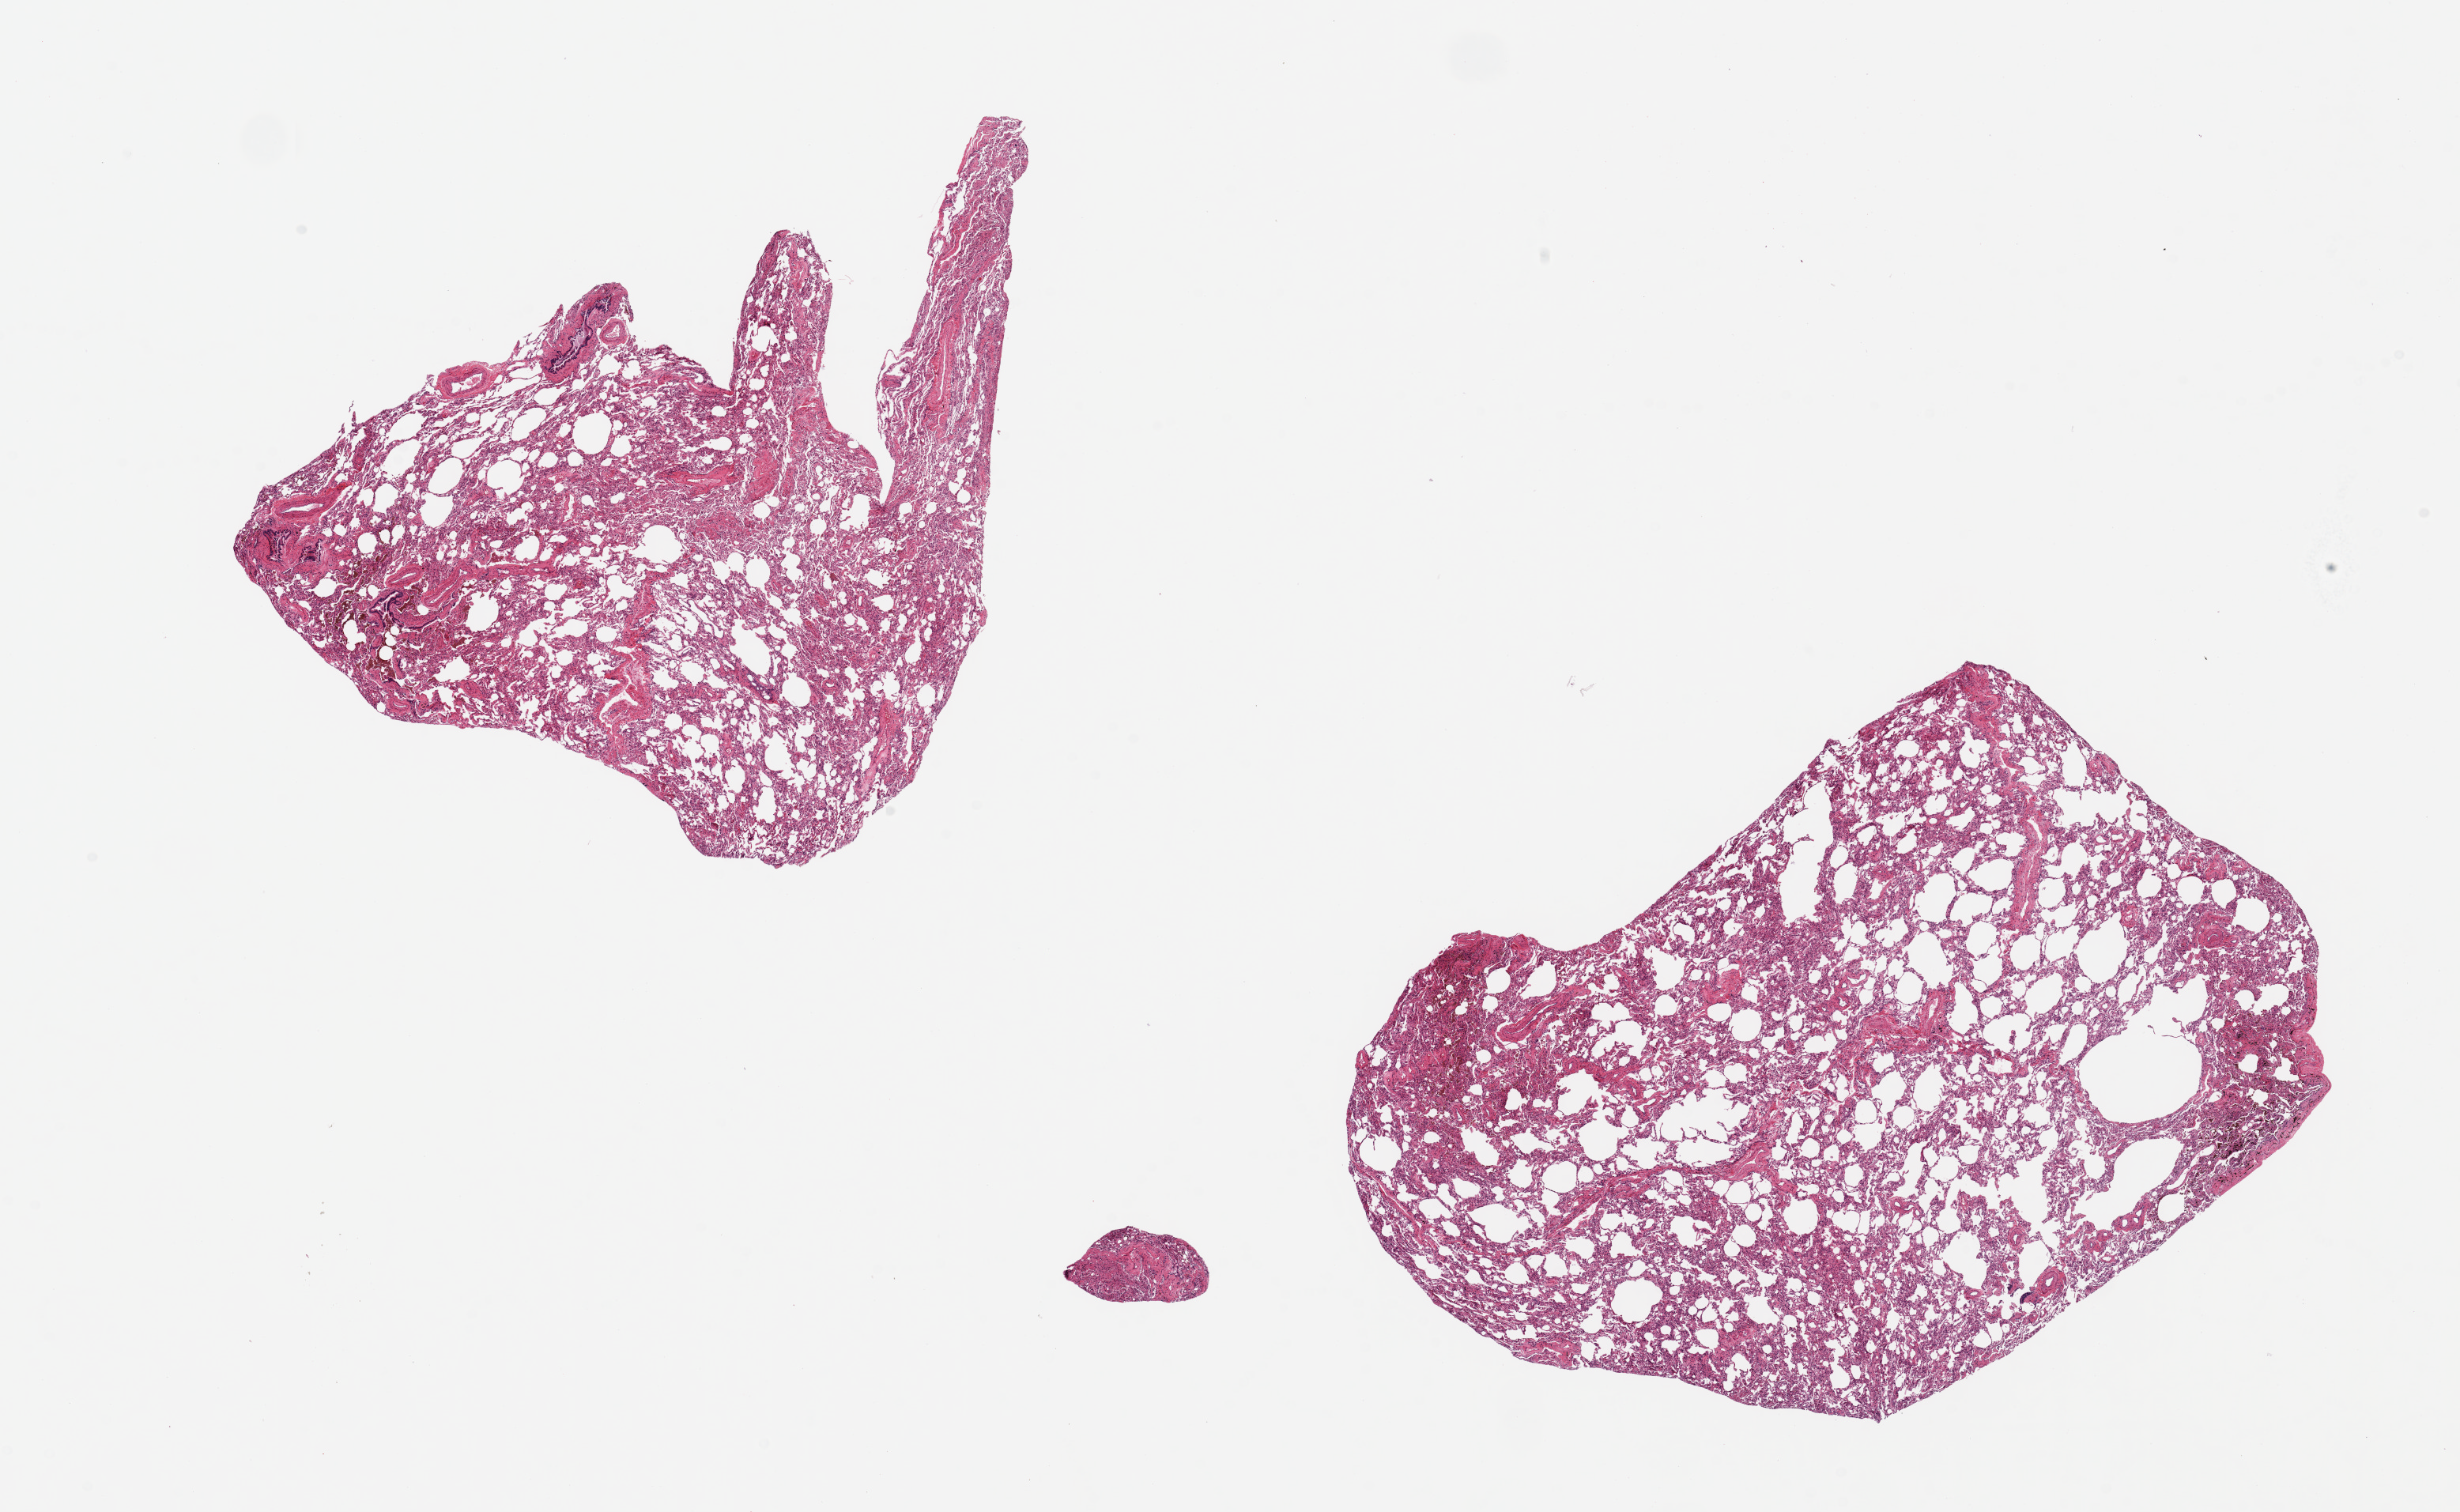
Digitized H&E-stained section, brightfield — shown as a low-resolution overview of the whole scanned area (about 24.6 x 15.1 mm, from a 20x scan); PAXgene-fixed, paraffin-embedded tissue; target tissue: lung; tissue donor sample. Donor sex: male.
Pathologist's review note for this sample: 2 pieces ~7x6mm. Emphysematous changes noted.